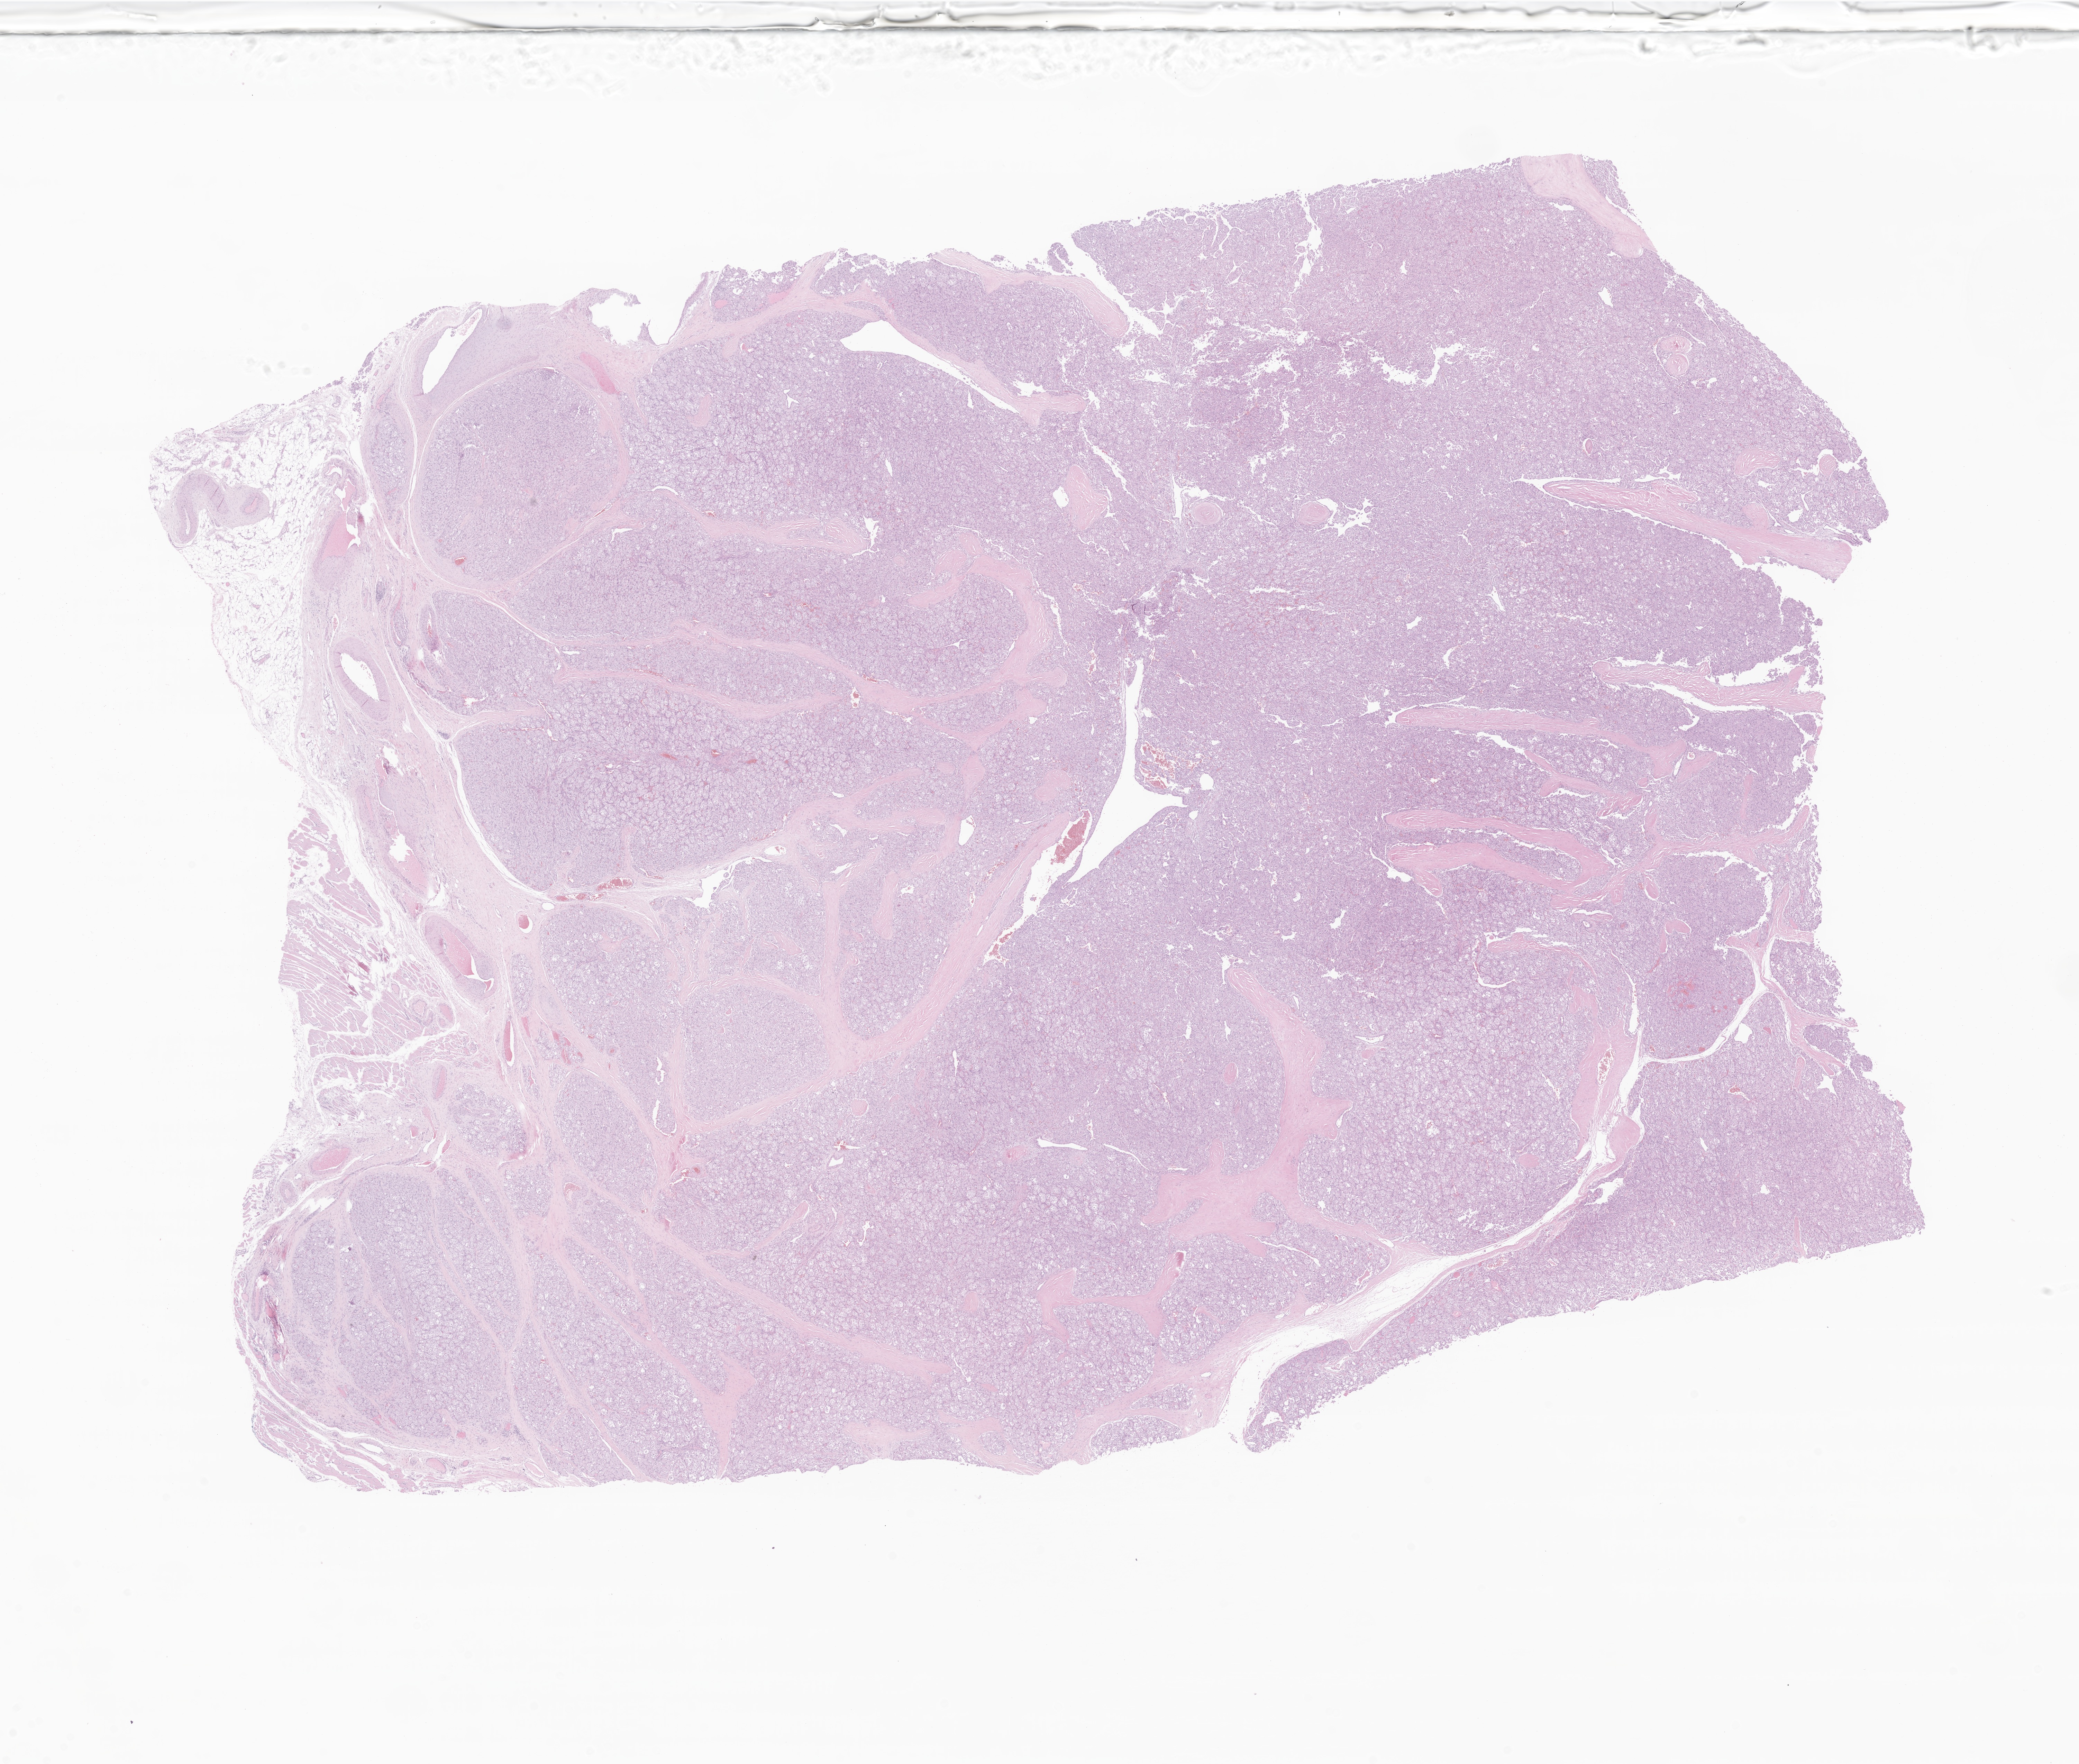
Digitized haematoxylin and eosin-stained section of tumor tissue from the lower limb — a low-resolution overview of the entire scanned area, about 25.3 x 21.5 mm. Formalin-fixed paraffin-embedded section. Patient: female, age 66 months (5 years 6 months).
• recorded diagnosis: Alveolar soft part sarcoma